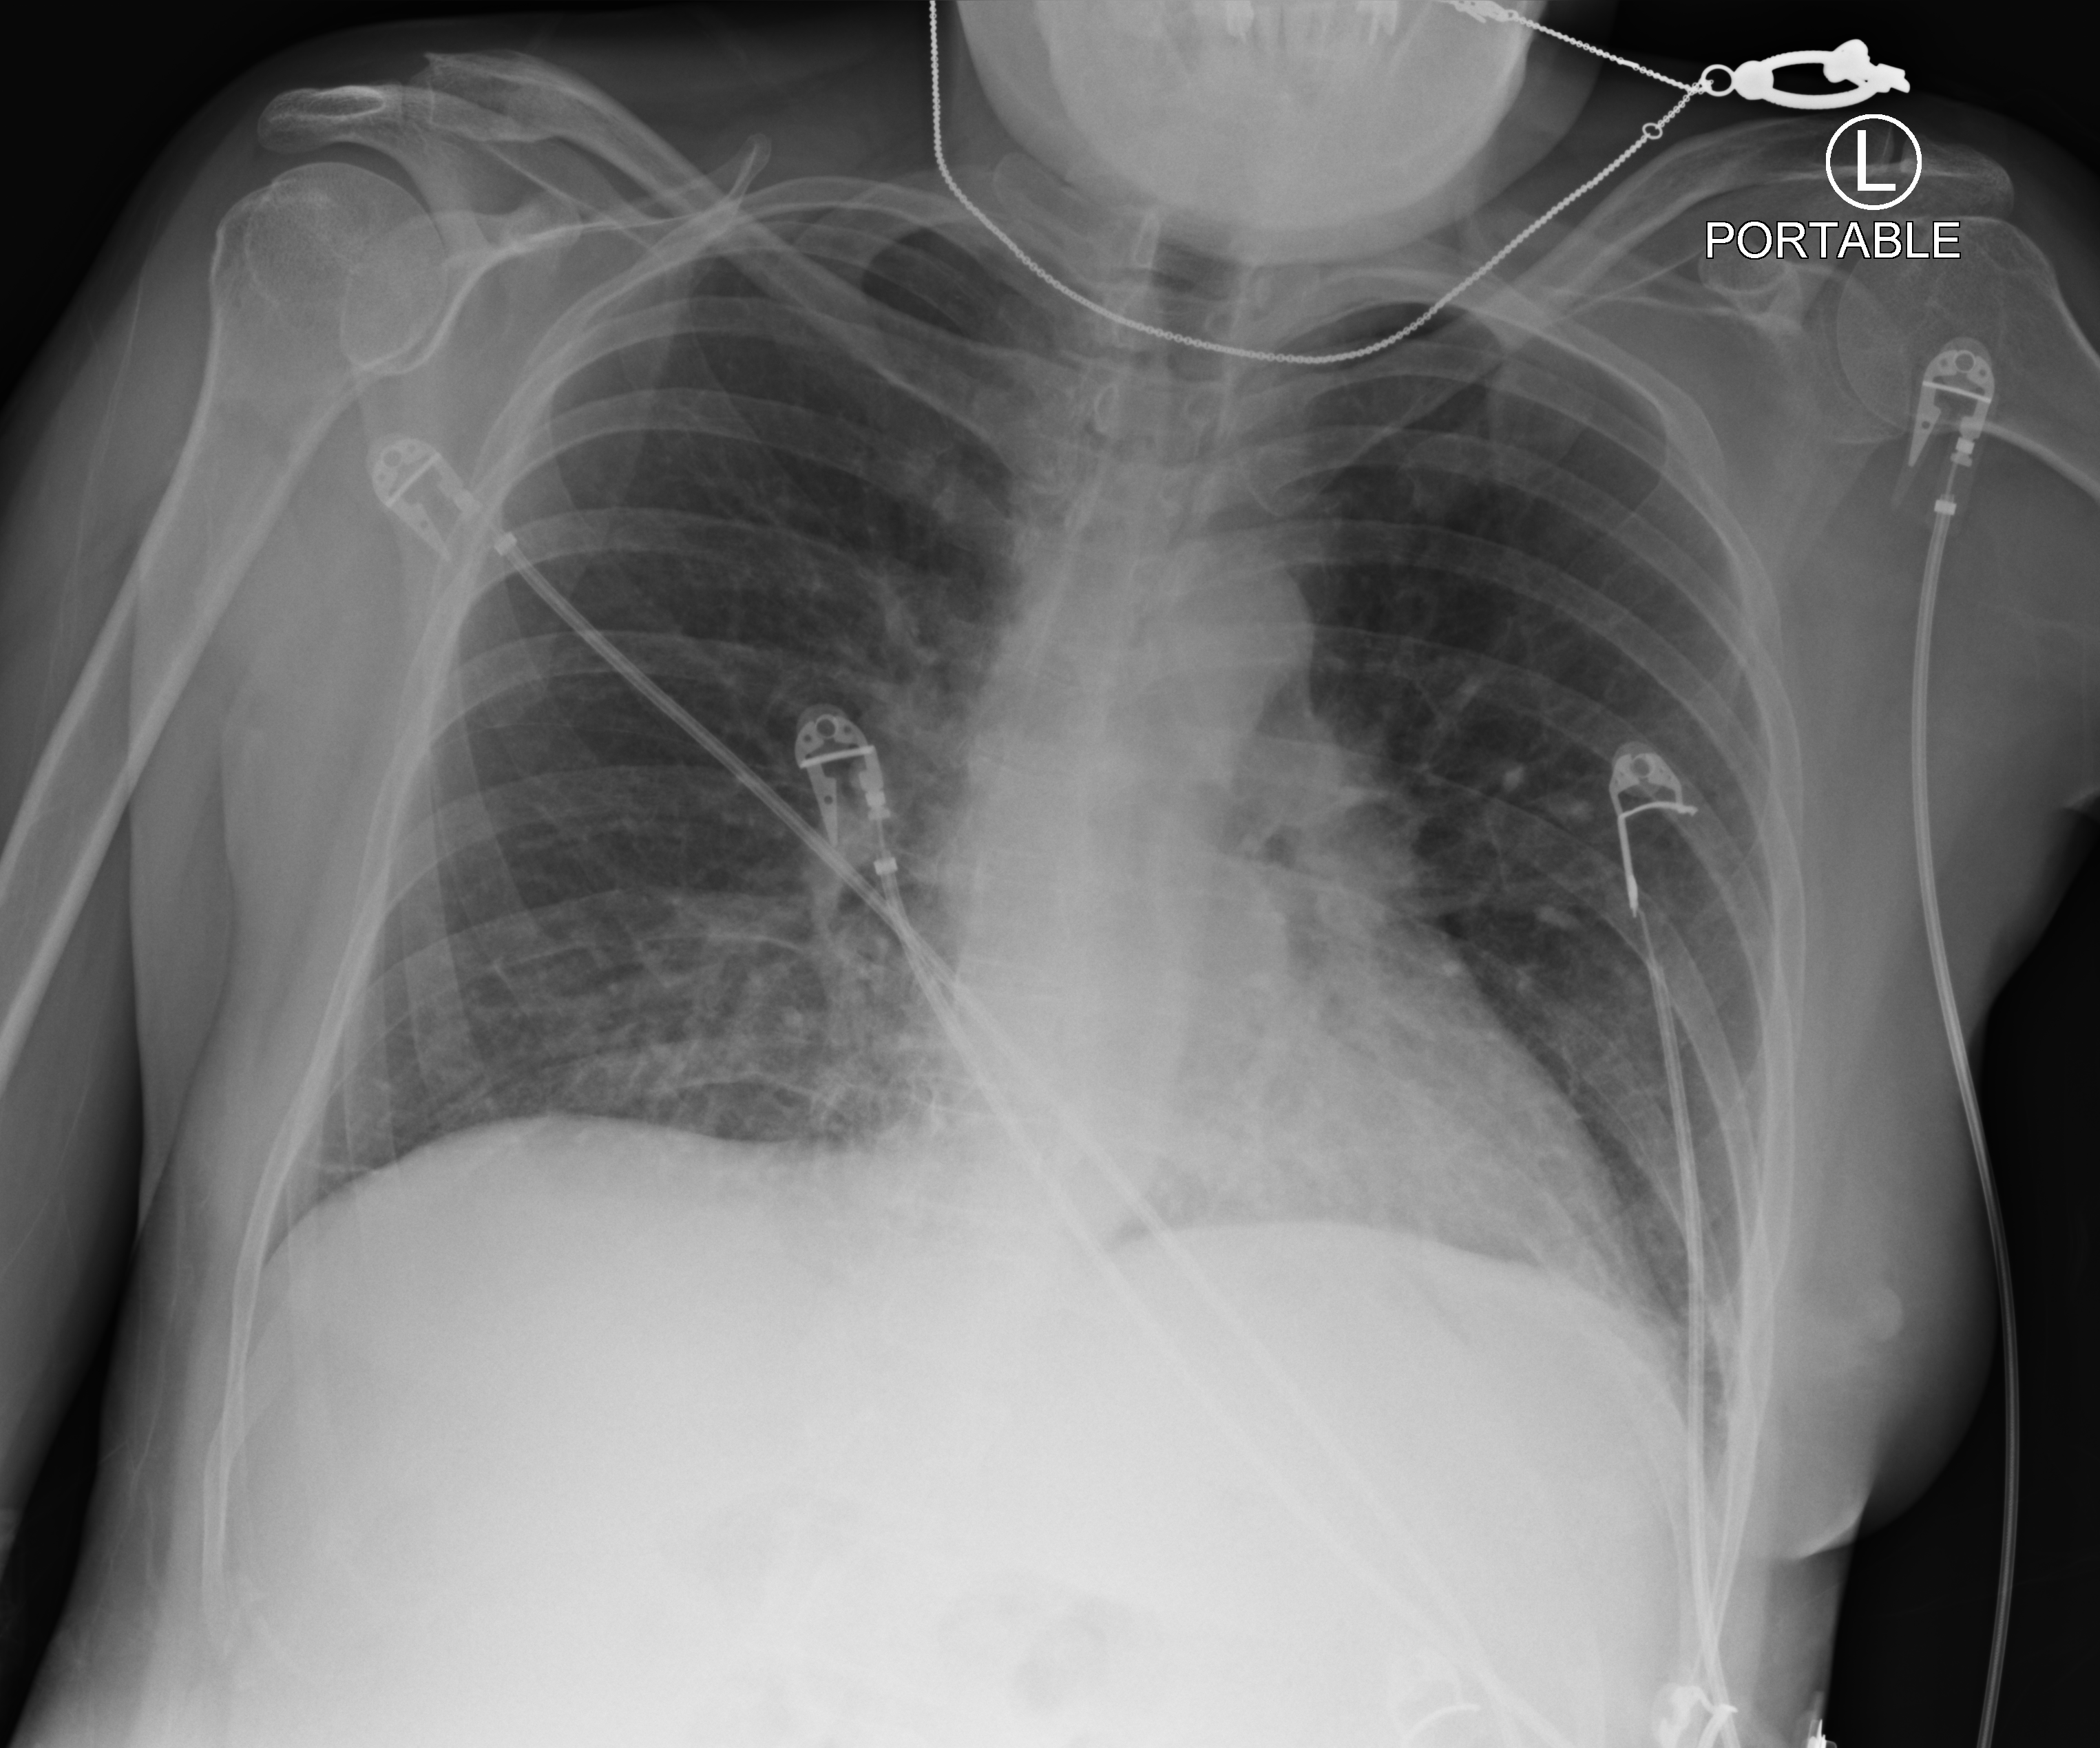
Chest X-ray (portable), anteroposterior (AP) projection. Patient hospitalised with COVID-19; female, aged 18–59 years.
Hospital-stay facts (about this admission, not read from this image; timing relative to this image not recorded): smoking status (admission record): never.